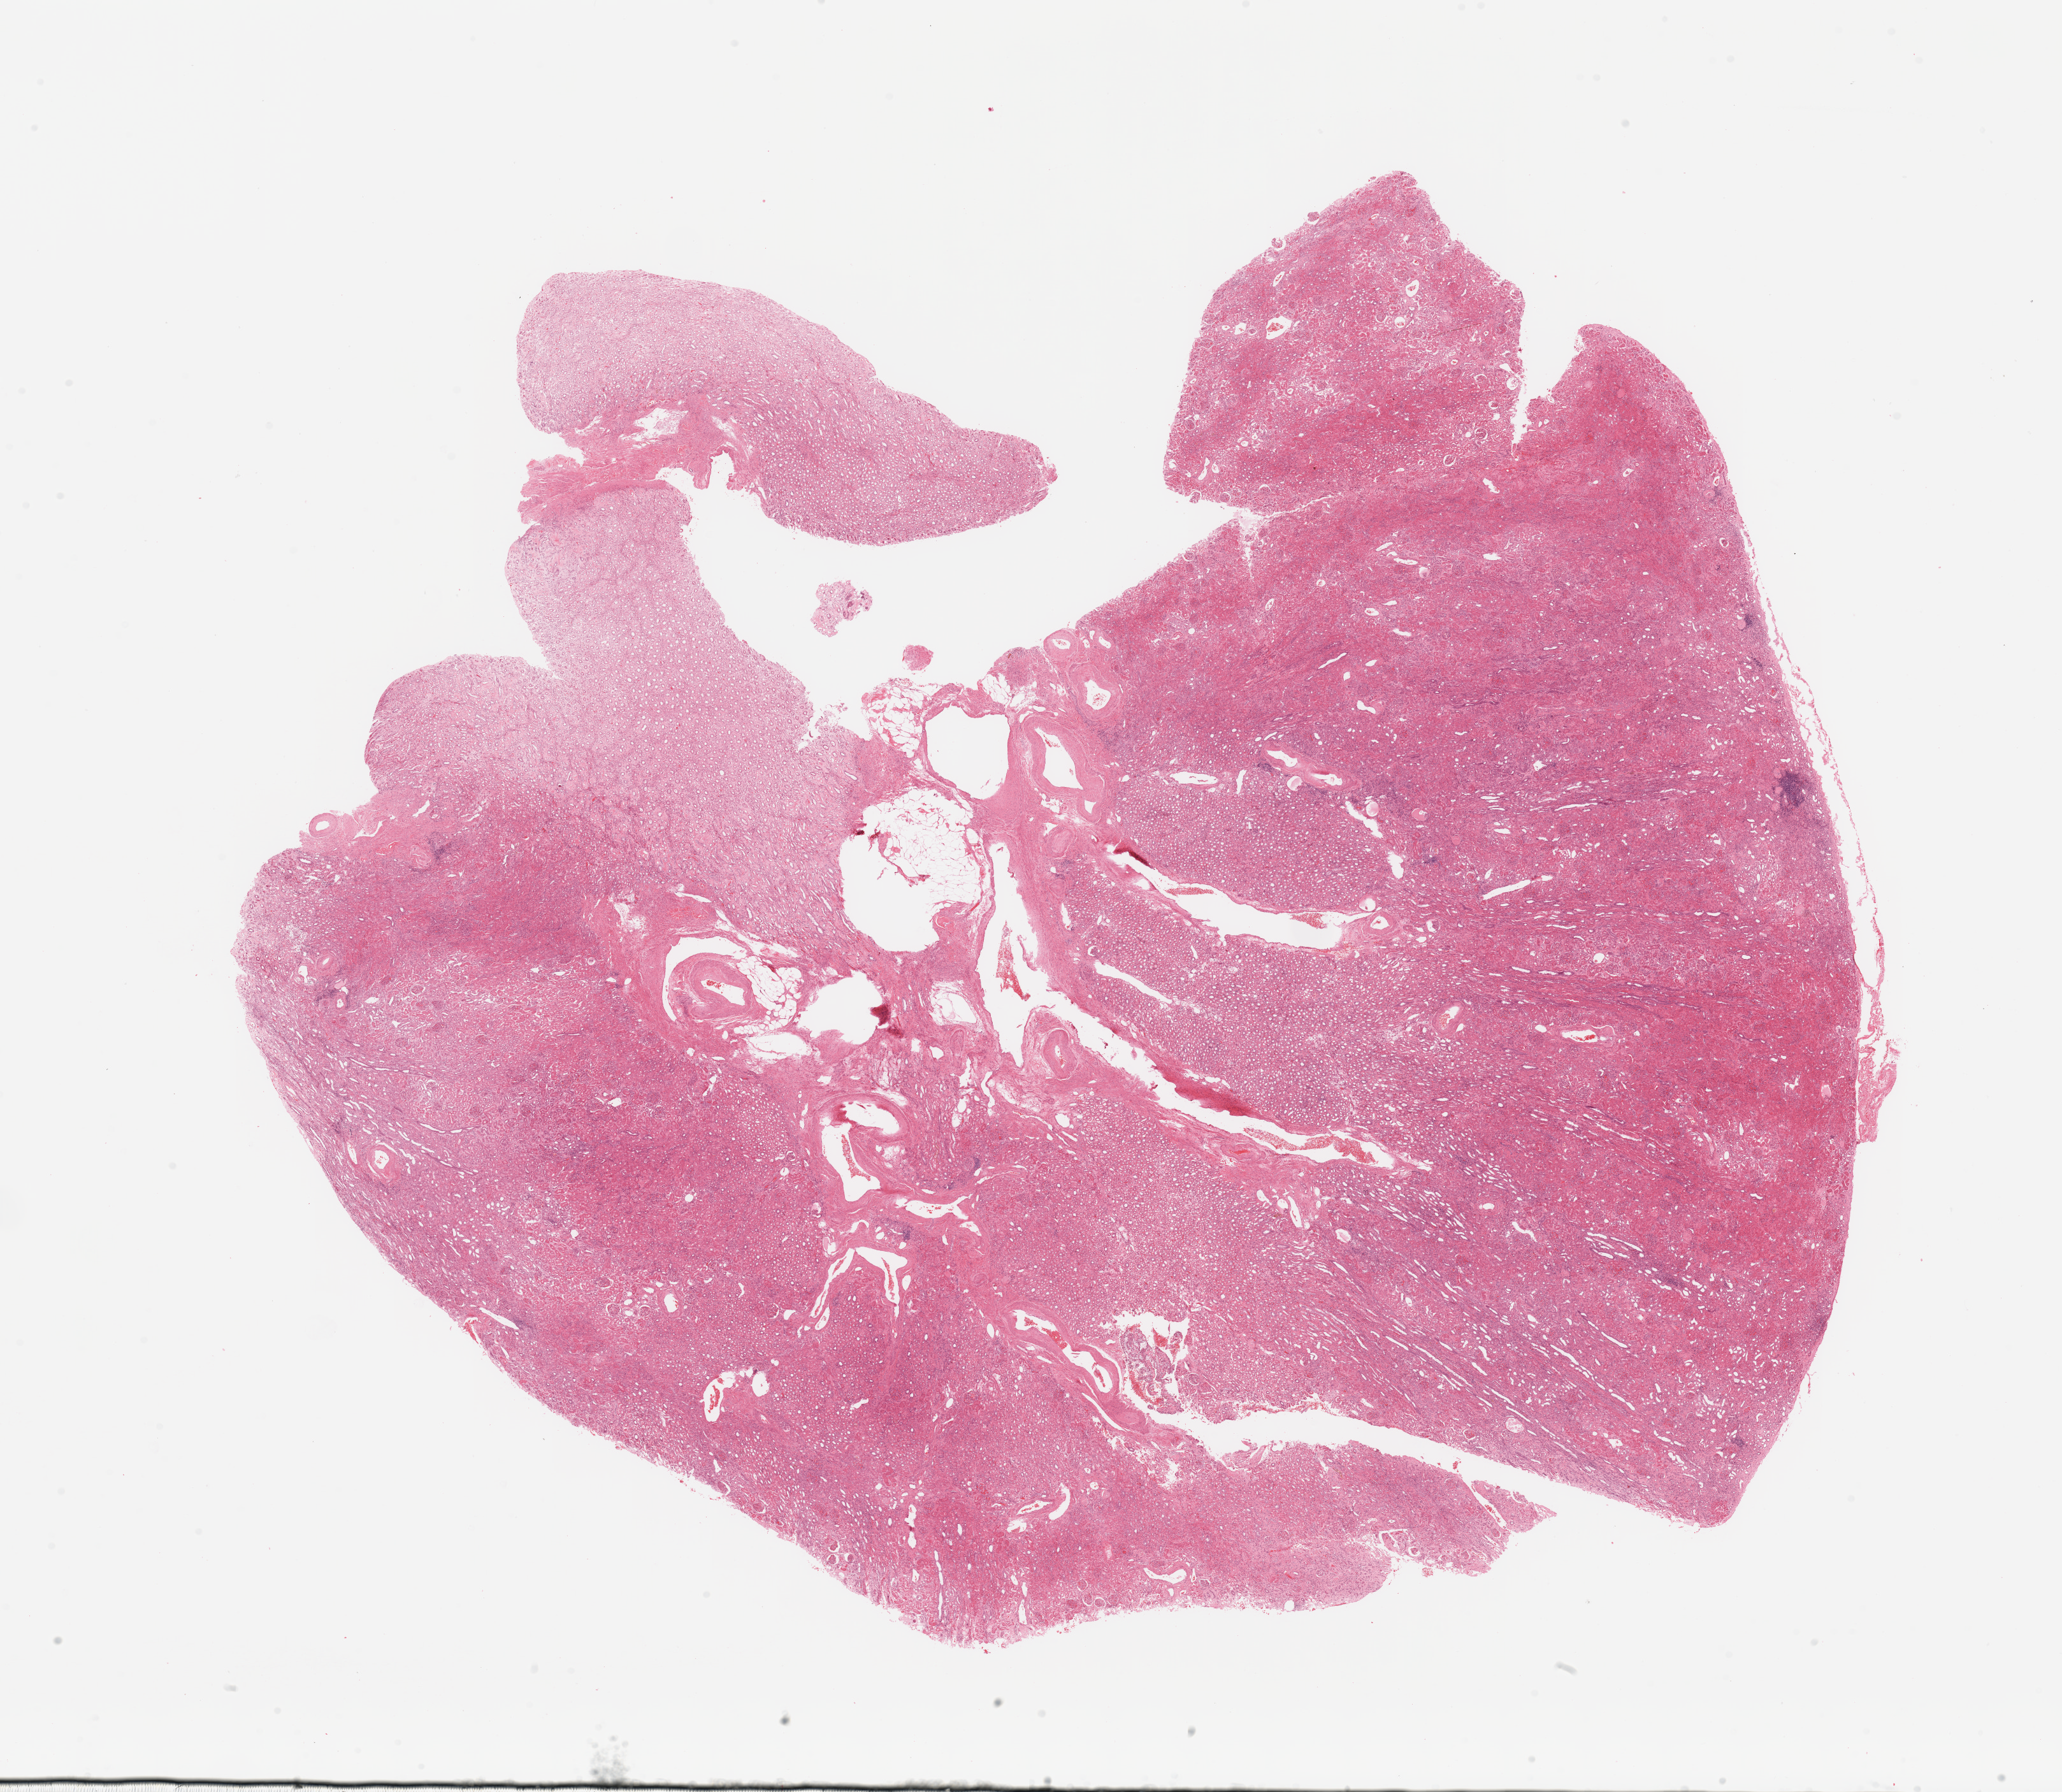
Whole-slide histology image, H&E-stained — shown as a low-resolution overview of the whole scanned area (about 25.6 x 22.2 mm, from a 20x scan), kidney, normal (non-tumour) tissue. Male, 66 y/o.
This section: normal (non-tumour) tissue from the same patient. Patient diagnosis: Renal cell carcinoma, NOS.